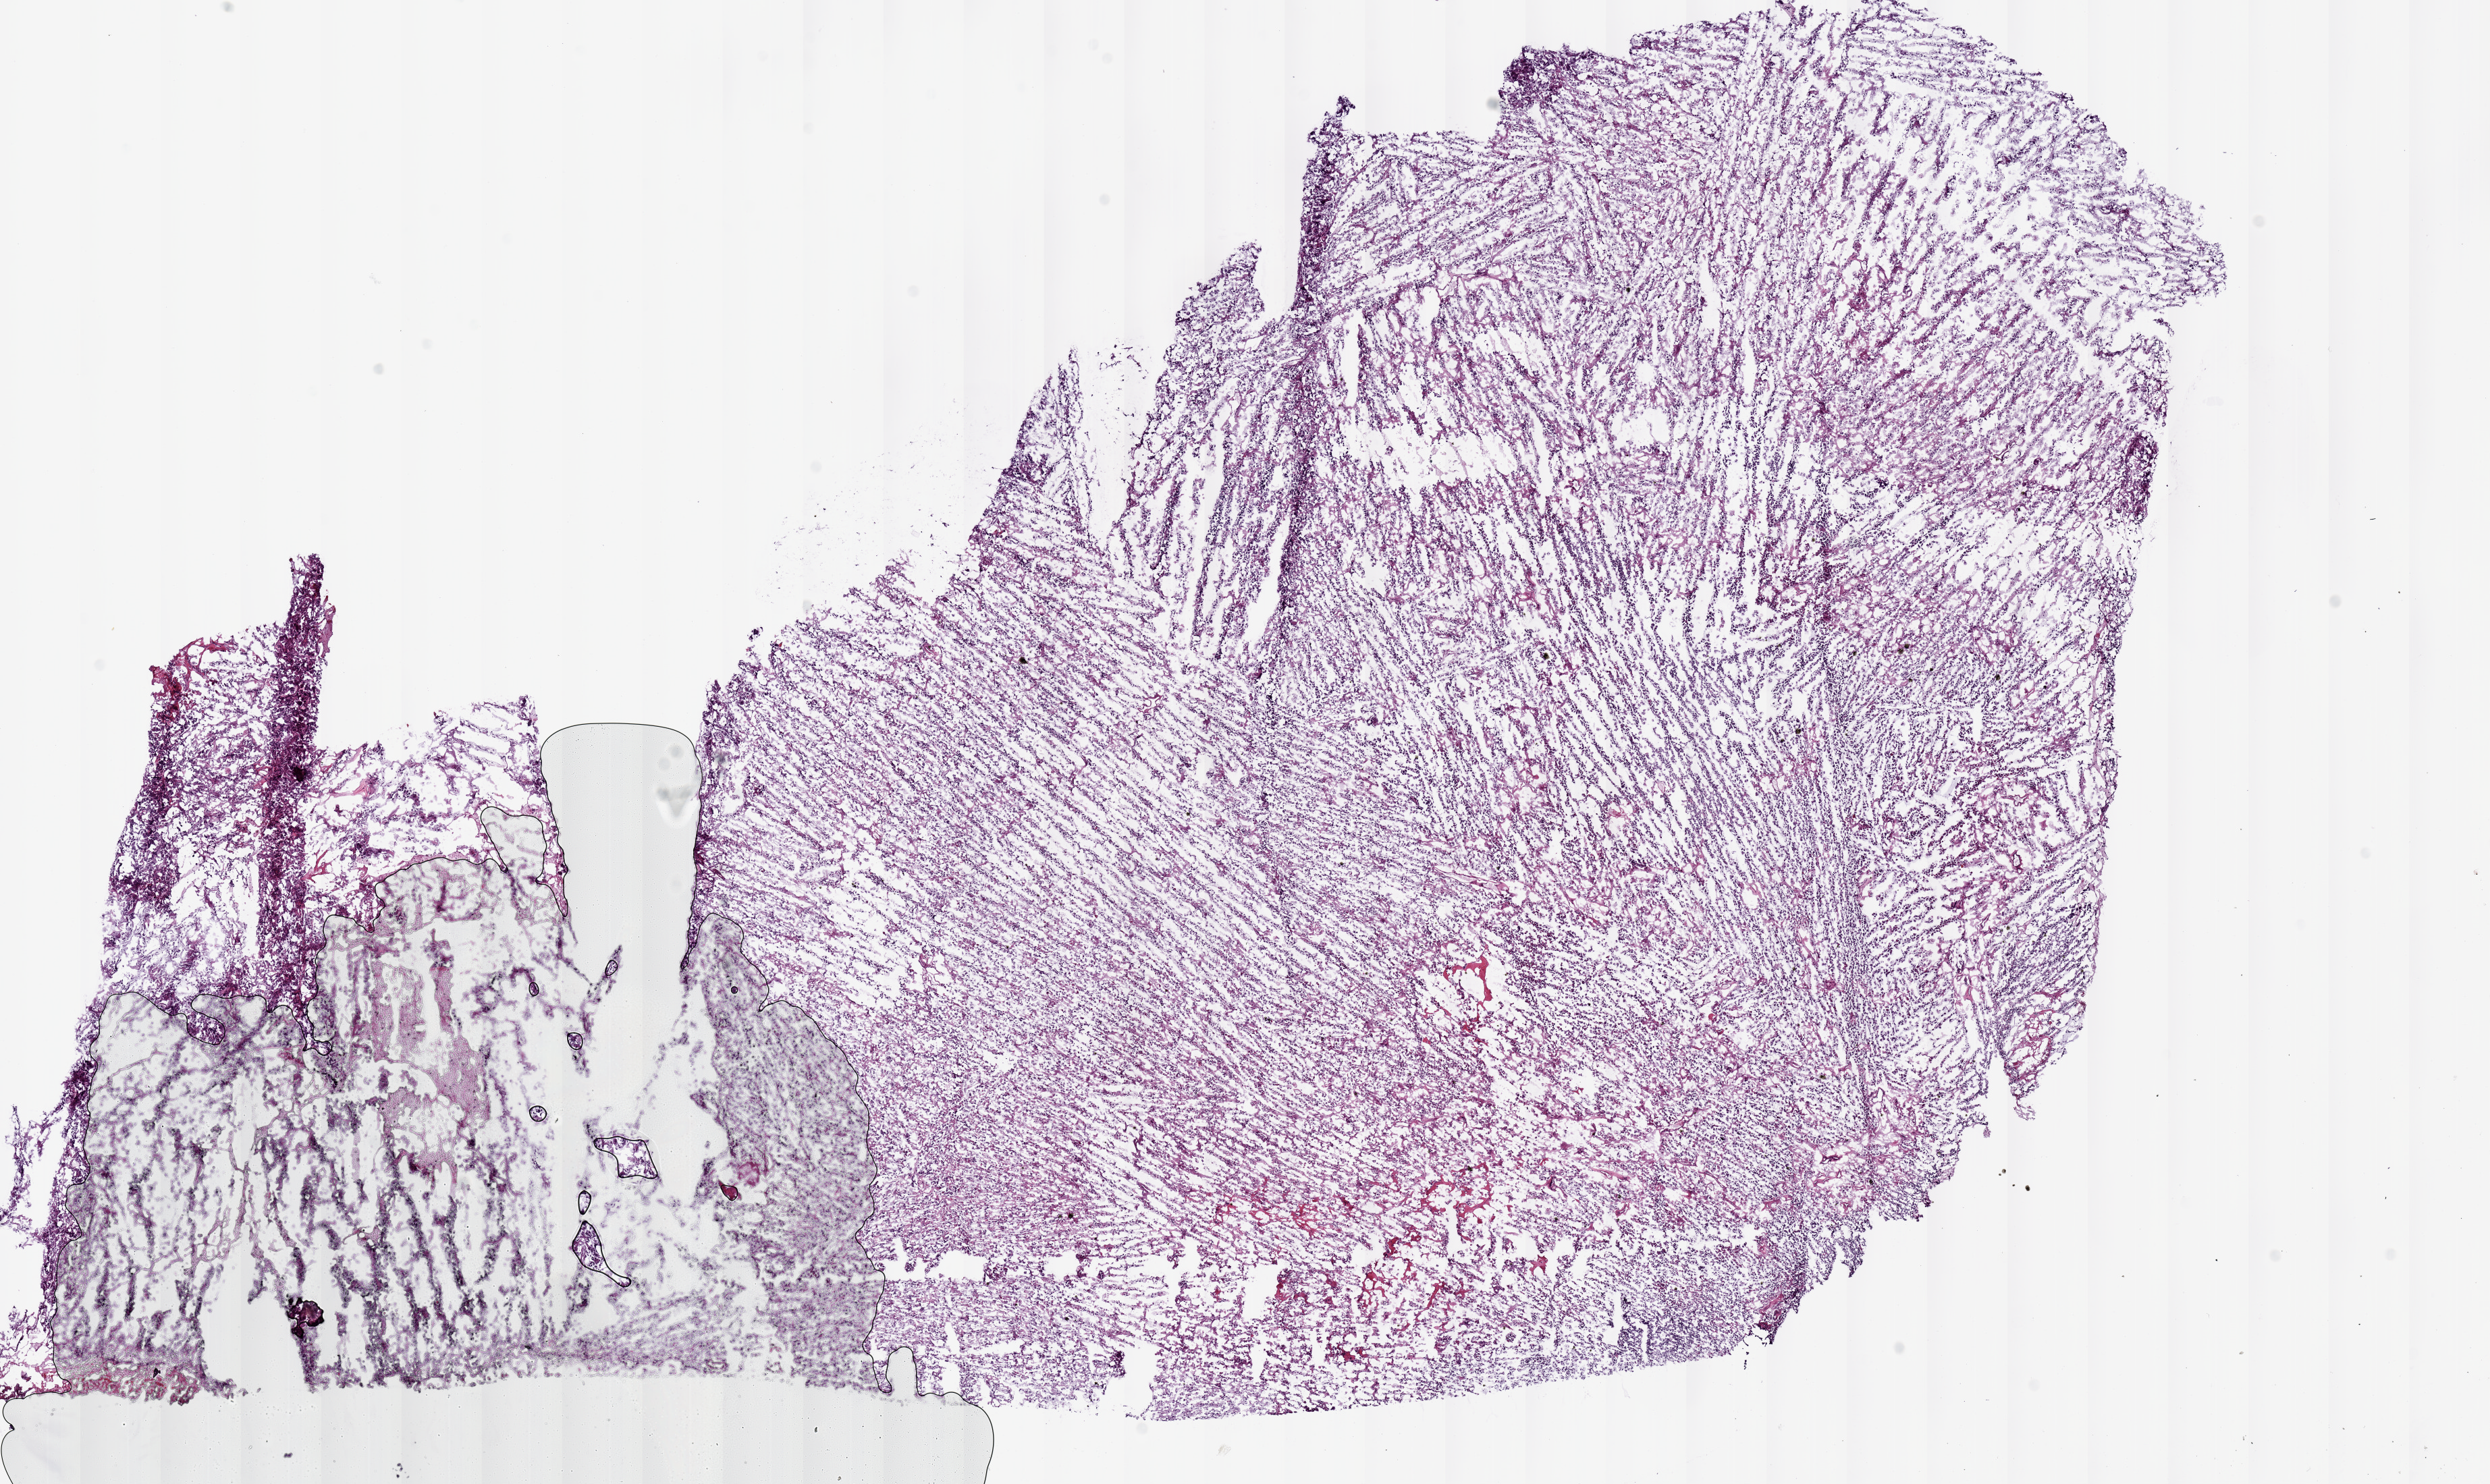
Digitized H&E tissue section (whole slide), low-resolution overview of the scanned area, about 14.6 x 8.7 mm, frozen section from the bottom of the tissue portion, sample: primary tumour, brain. Female, age 53 years at initial diagnosis. Pathologist review of this section (percent, as recorded): tumour cells 100%, tumour nuclei 85%.
Diagnosis: Oligodendroglioma, anaplastic.